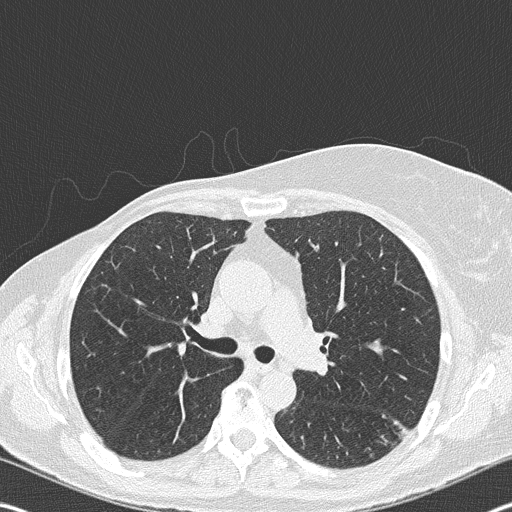
Low-dose screening chest CT, one axial slice; position 115 of 177 along the scan axis; 120 kVp; lung window (W 1500 / L -600 HU); 512 × 512 image matrix, field of view 342 × 342 mm.
Structures marked on this image (expert manual segmentation):
- lesion 1 (tumor): bounding box [x1, y1, x2, y2] px = [398, 422, 407, 436]